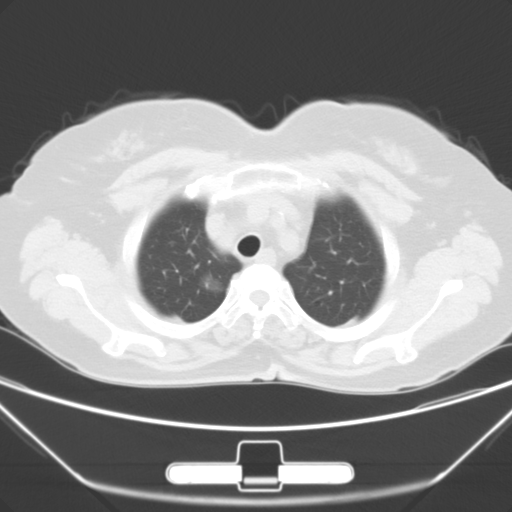
Chest CT, one axial slice; position 47 of 55 along the scan axis; 120 kVp; lung window (W 1500 / L -600 HU); 512 × 512 image matrix, field of view 356 × 356 mm. Patient: female, 63 years. Case-level facts recorded for this patient, not image findings: clinical TNM (as recorded): T1a N0 M0; histopathological grade: G1.
Structures marked on this image (bounding box drawn by a radiologist):
- lung tumour (recorded histology: adenocarcinoma): box from (x=189, y=266) to (x=223, y=297) px